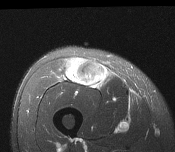
MRI of an extremity soft-tissue mass, one axial slice. Position 60 of 116 along the scan axis. T2-weighted fat-saturated. MR volume resampled by the dataset authors to the PET/CT grid (not the native acquisition matrix). 3.27 mm slice thickness. 175 × 152 image matrix, field of view 171 × 148 mm. Male patient. From the clinical record (not read from this slice): histological type: pleiomorphic leiomyosarcoma; grade: intermediate; site of the primary tumour: right thigh.
Structures marked on this image (expert contour drawn on MRI and transferred to this co-registered scan by the dataset authors):
- gross tumour volume including surrounding oedema: bounding box (x1, y1, x2, y2) in pixels: (67, 58, 110, 89)